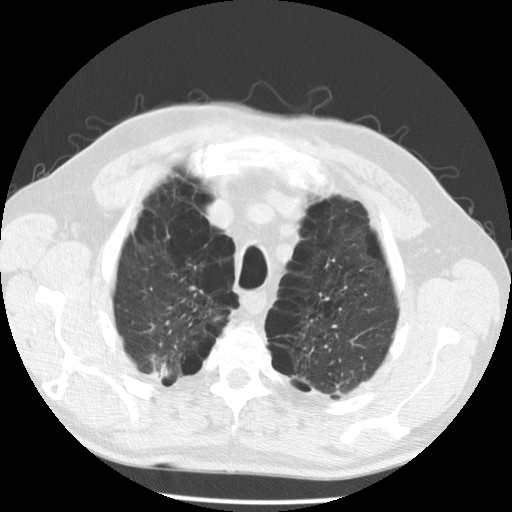
Chest CT (low-dose screening protocol), one axial image. Second annual screen. Lung window (W 1500 / L -600 HU). 120 kVp. Slice 29 of 167 in the series. 512 × 512 image matrix. Male participant, aged 68 years at enrolment.
Expert-annotated lung lesion, box from (x=121, y=314) to (x=196, y=392) px. The screening reader recorded 2 non-calcified nodules or masses ≥4 mm on this exam (lingula, left lower lobe); which of them this box marks is not recorded. Official screen result: positive, no significant change: stable abnormalities potentially related to lung cancer, unchanged since the prior screening exam. Later outcome: lung cancer diagnosed 617 days after this screen — large cell carcinoma, NOS, right upper lobe, poorly differentiated (G3), stage IV (AJCC 6th edition).